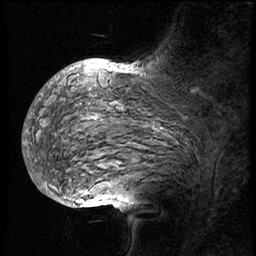
Breast MRI (dynamic contrast-enhanced), one sagittal slice. Slice 37 of 56 in the series (ordered by position). 3 images stored at this slice position (order not interpretable as contrast timing). 1.5 T. TE 4.2 ms, TR 8.9 ms. 3 mm slice thickness. 256 × 256 image matrix. Female patient, age 57 years. Case-level facts recorded for this patient, not image findings: setting: breast cancer imaged before/during neoadjuvant chemotherapy; receptor status: HER2-positive.
Outlined on this slice (semi-automatically segmented with operator editing):
- analysis volume of interest (the breast-tissue region the enhancement analysis was run in; not a lesion): bounding box [x1, y1, x2, y2] px = [28, 70, 228, 156]
- tumour enhancement mask (voxels above the 140 % enhancement threshold inside the analysis volume of interest): [91, 71, 131, 119]